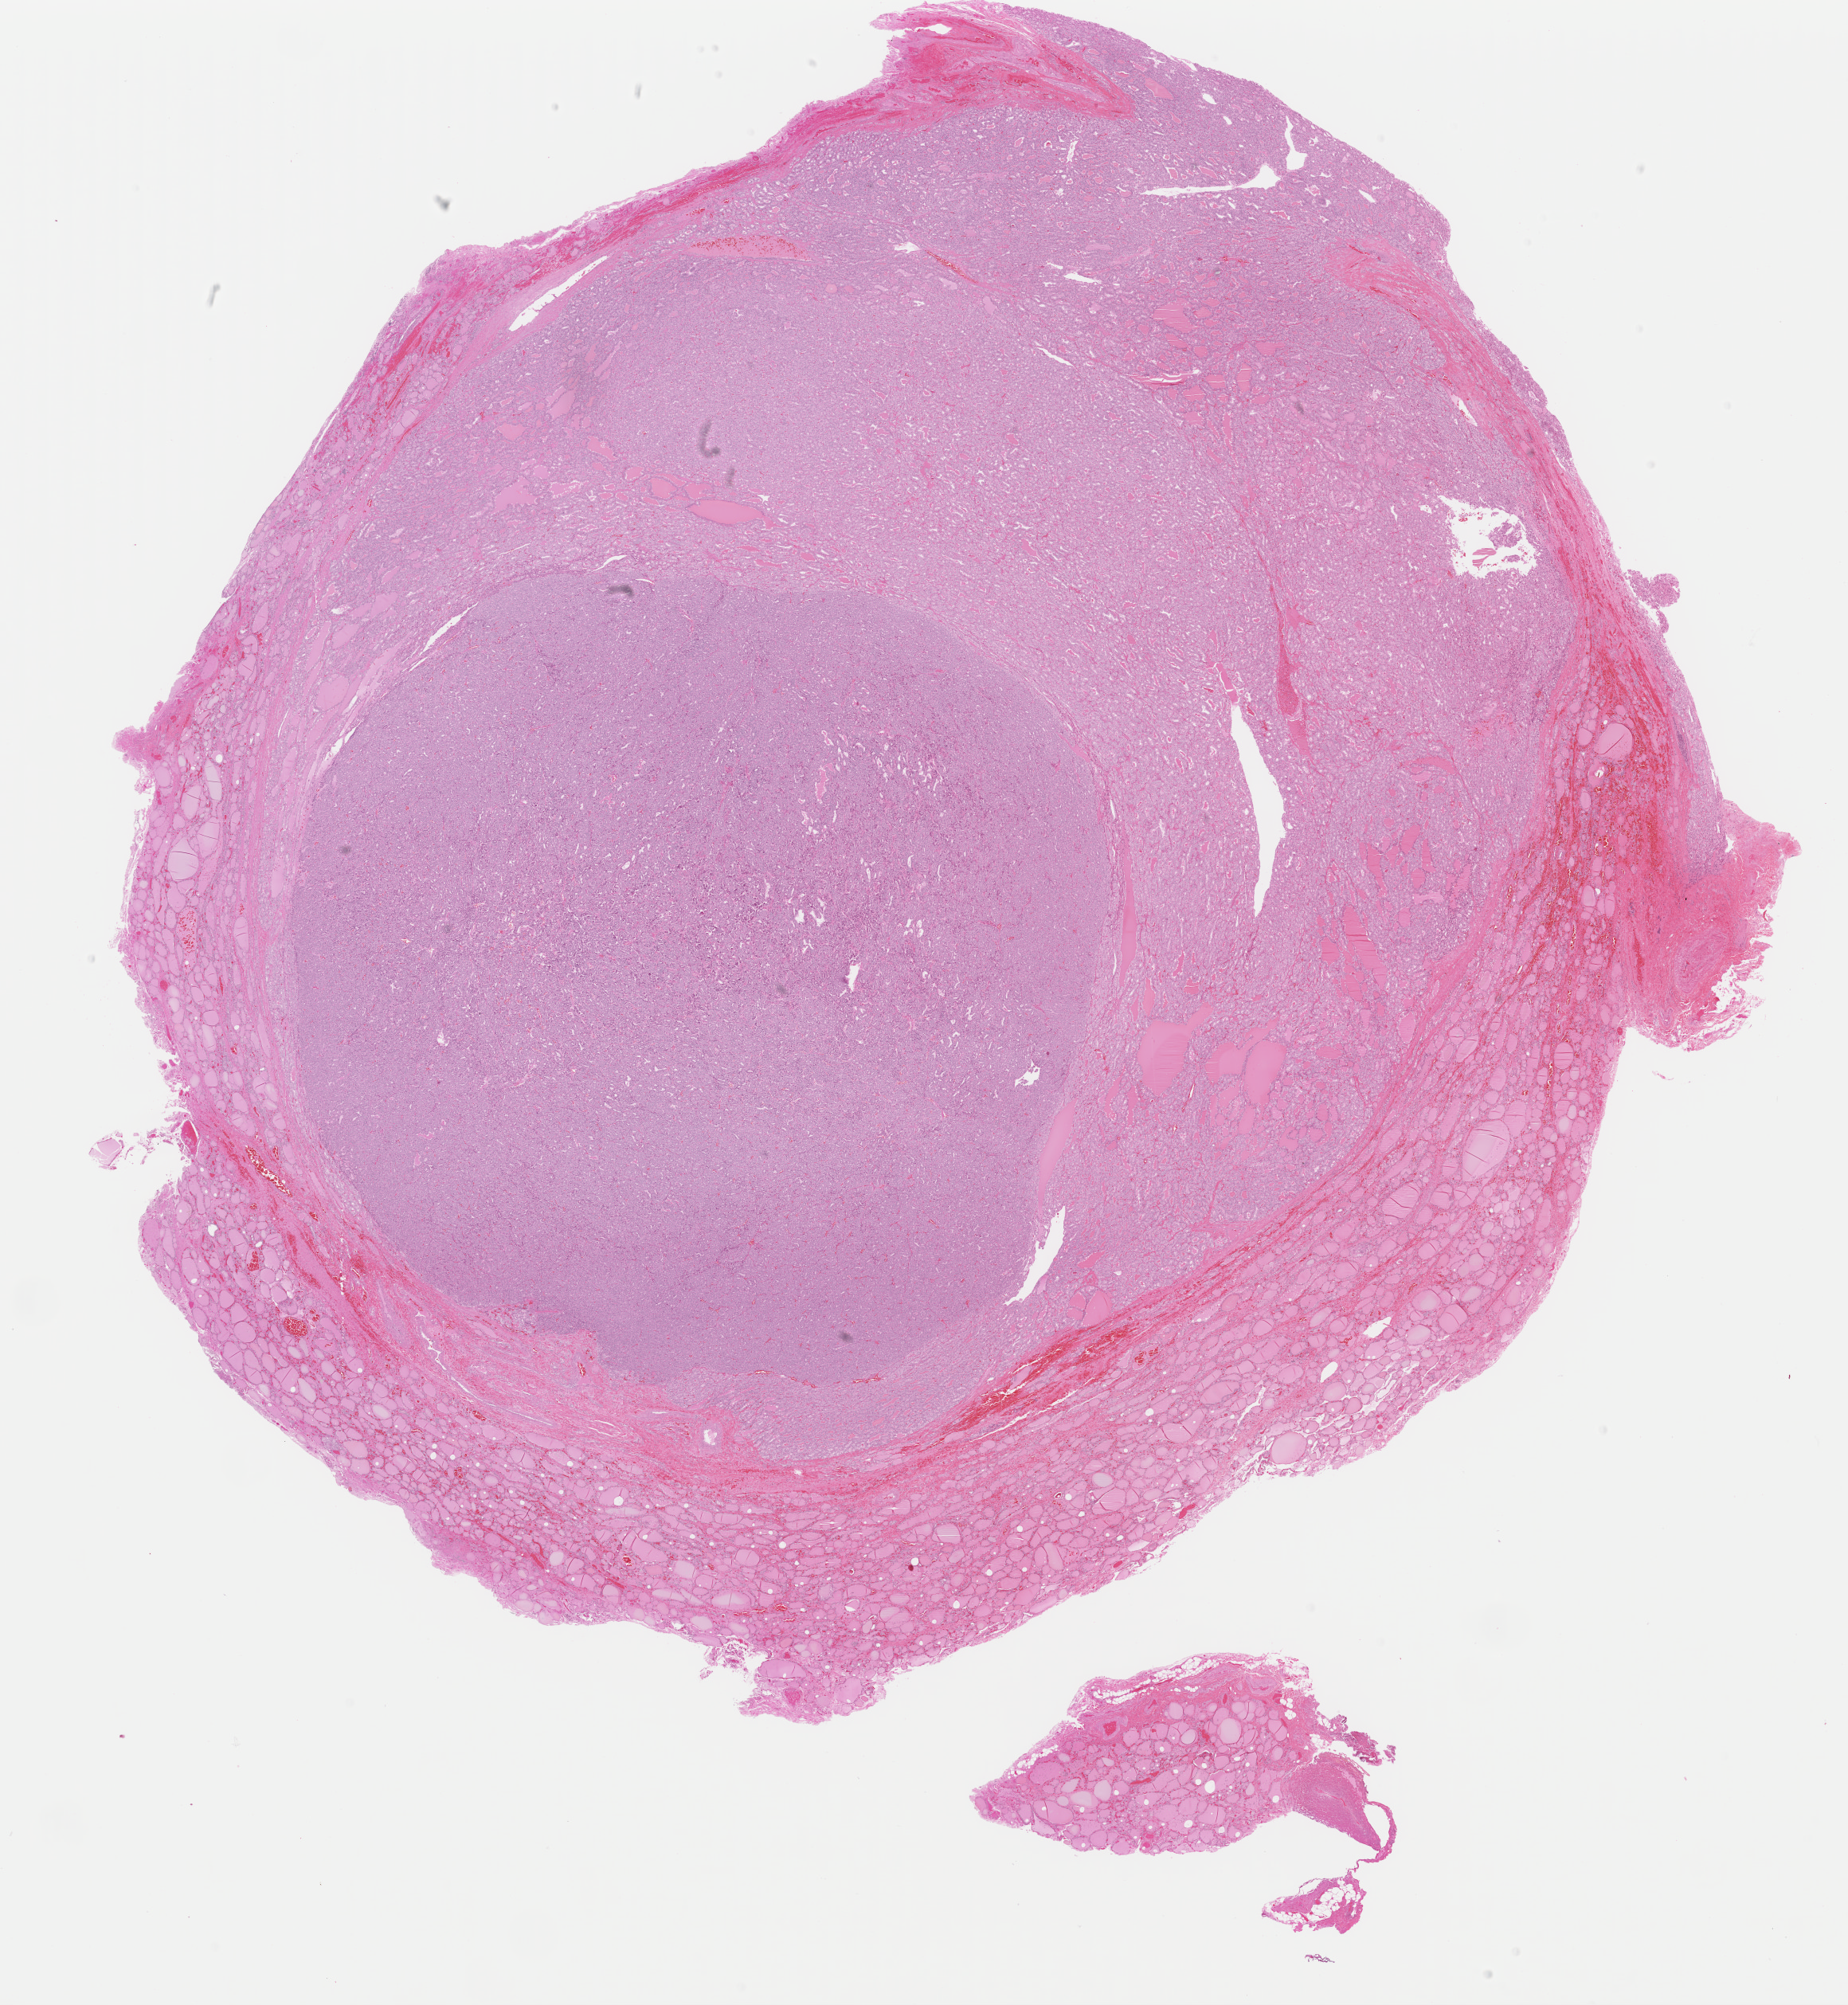
Digitized H&E tissue section (whole slide), a low-resolution overview of the entire scanned area, about 18.3 x 19.9 mm (acquisition: 40x scan). Formalin-fixed paraffin-embedded (FFPE) diagnostic section. Primary tumour sample from the thyroid. Female patient; age at initial diagnosis 46 years.
Histologic diagnosis: Papillary adenocarcinoma, NOS (thyroid gland). AJCC pathologic stage: II (6th edition).